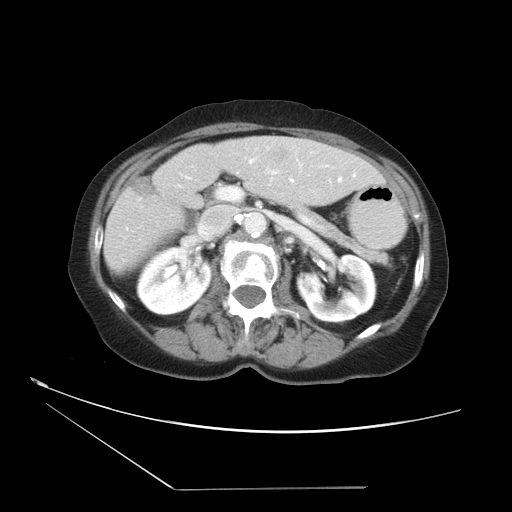
Contrast-enhanced abdominal CT, one axial slice. 120 kVp. Intravenous contrast given. Soft-tissue window (W 400 / L 40 HU). 5 mm slice thickness. 512 × 512 image matrix, field of view 384 × 384 mm. Female patient, age 81 years. From the clinical record (not read from this slice): diagnosis: colorectal cancer liver metastases, imaged before liver resection; multiple liver metastases: no; largest metastasis: 1.6 cm; disease in both lobes: no.
Annotated regions visible in this slice (outlined manually by an expert reader):
- hepatic veins: bounding box <250,161,341,182> (left, top, right, bottom; pixels)
- liver: <104,137,385,274>
- planned liver remnant (the part of the liver to remain after resection): <104,142,385,274>
- portal vein (with intrahepatic branches): <221,171,275,199>
- liver metastasis: <261,141,292,167>